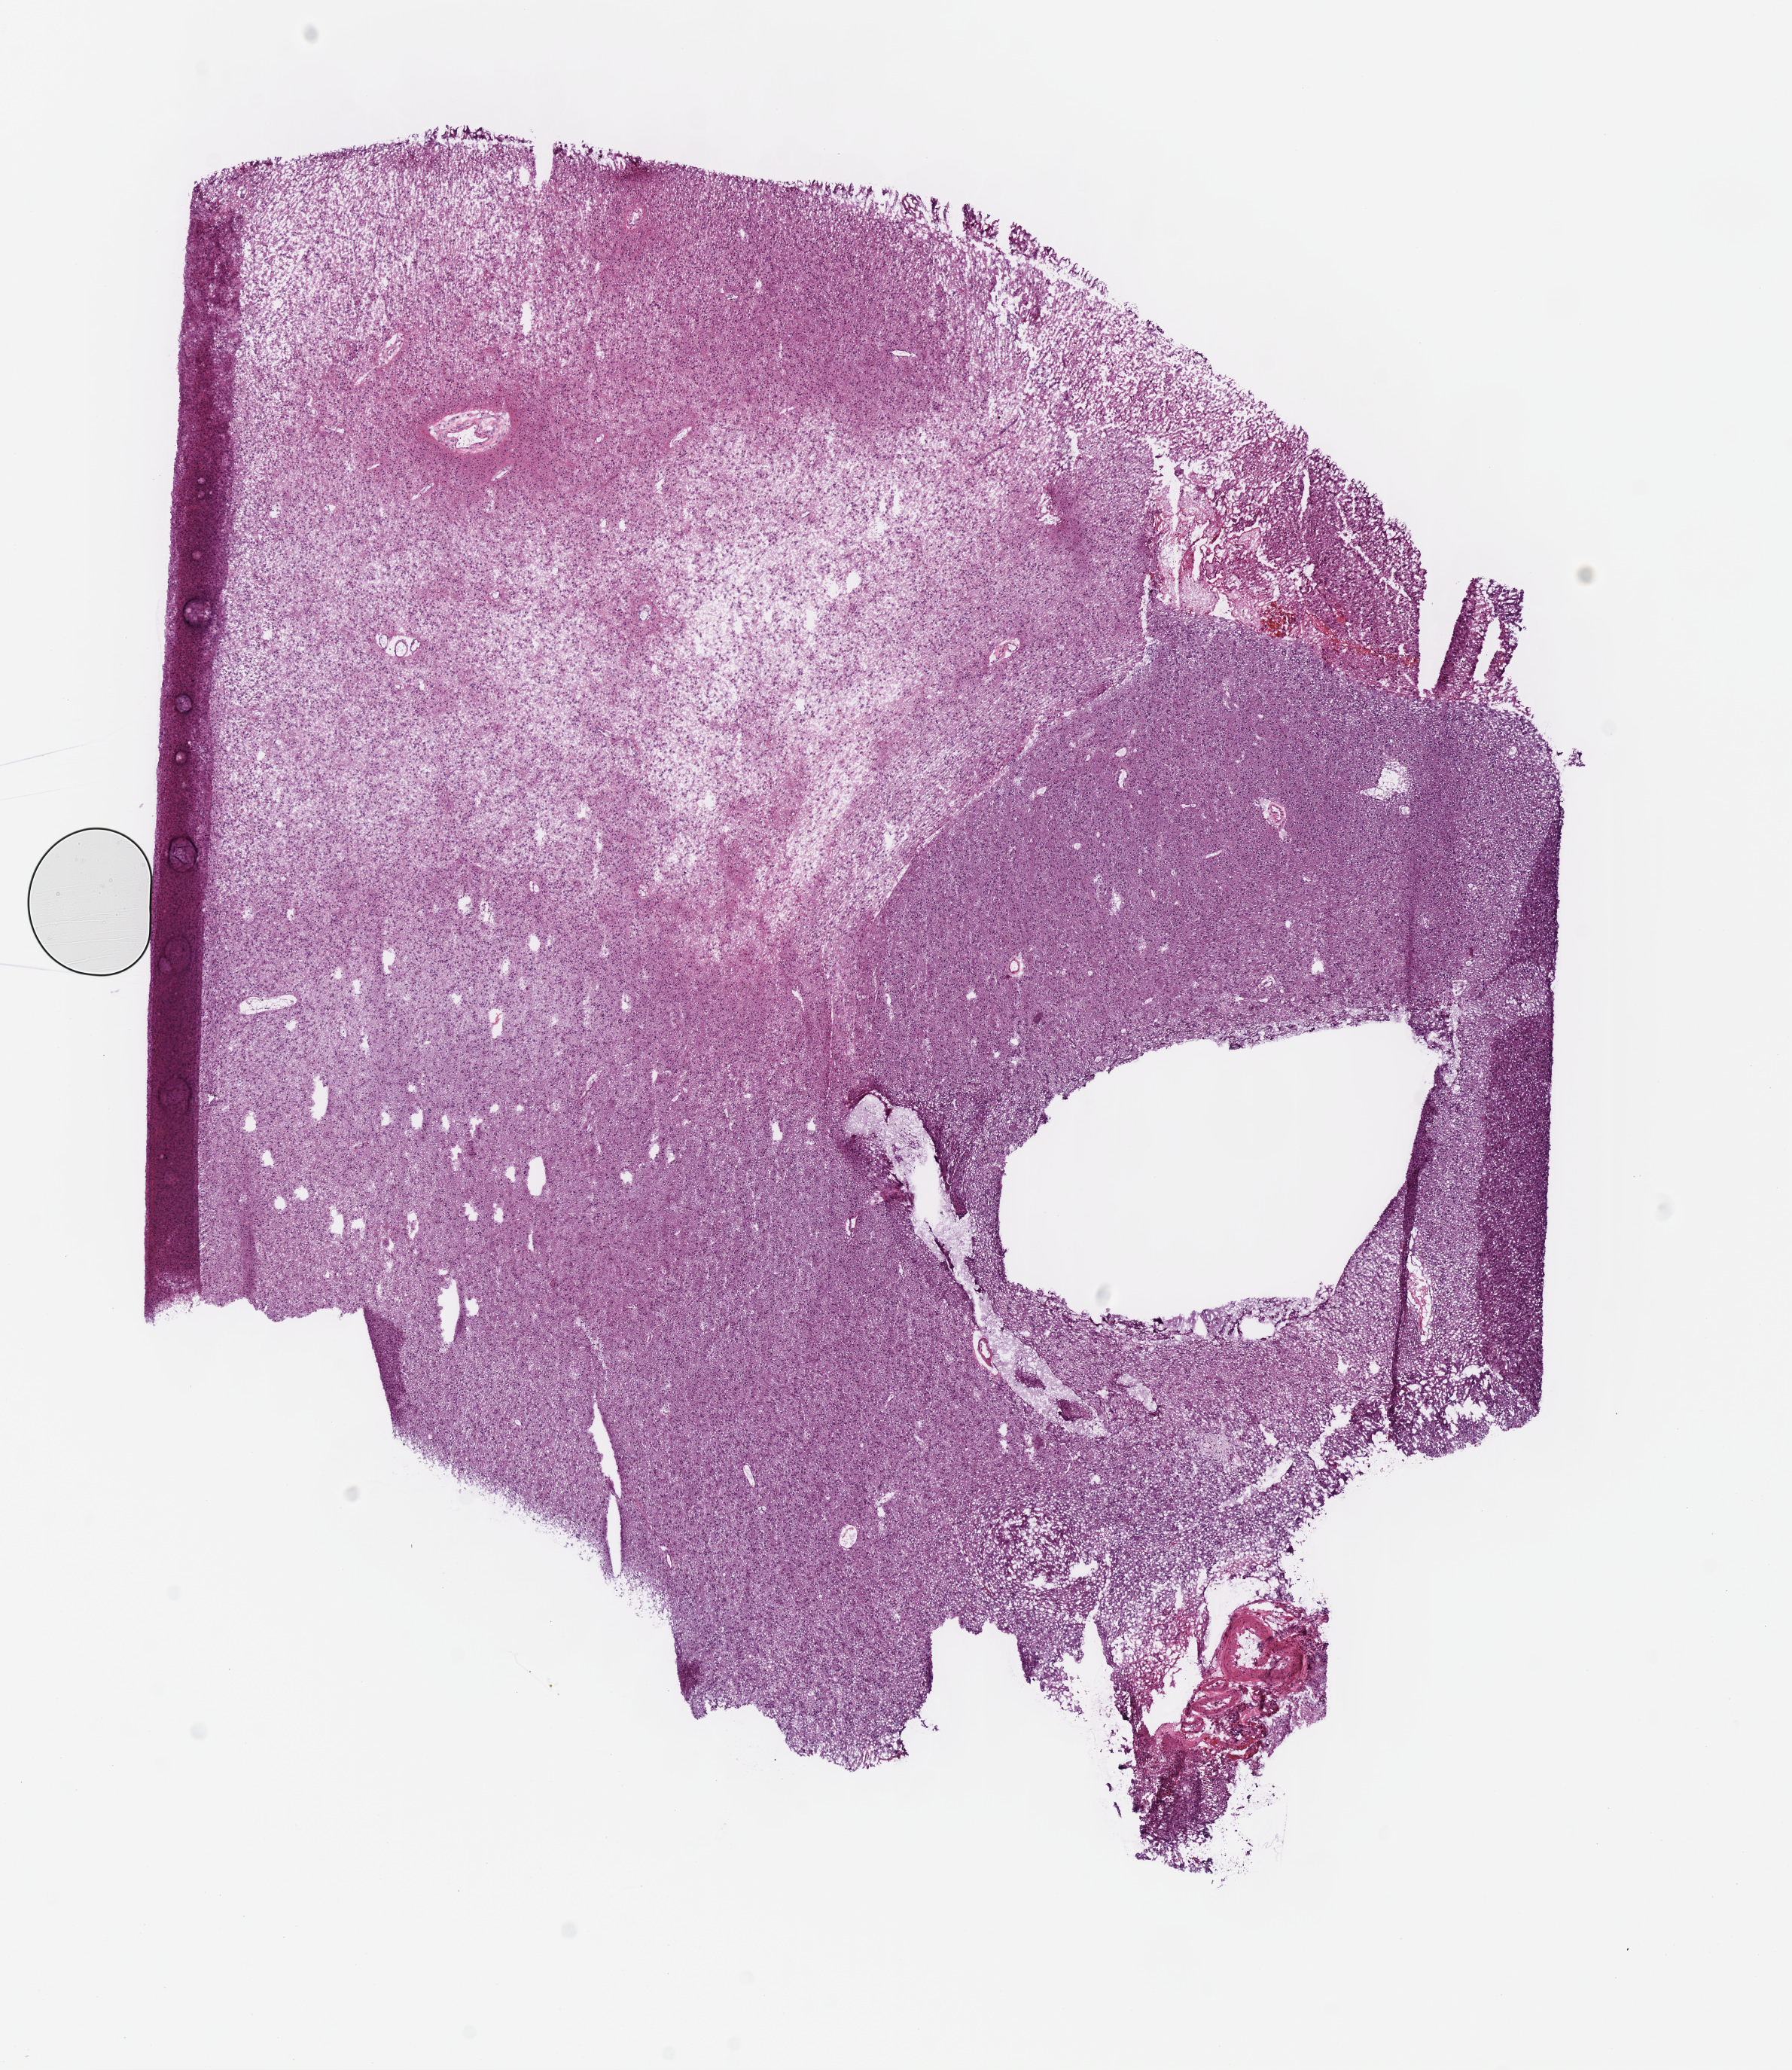
Whole-slide histology image, Hematoxylin and eosin (H&E) stained, low-resolution overview of the scanned area, about 9.4 x 10.8 mm. Frozen section from the top of the tissue portion. Brain, primary tumour sample. Patient: male, age at initial diagnosis 61 years. Histologic grade: G2 (moderately differentiated). Pathologist review of this section (percent, as recorded): tumour cells 100%, tumour nuclei 80%, normal cells 0%, stromal cells 0%, necrosis 0%.
Histologic diagnosis: Mixed glioma (cerebrum).